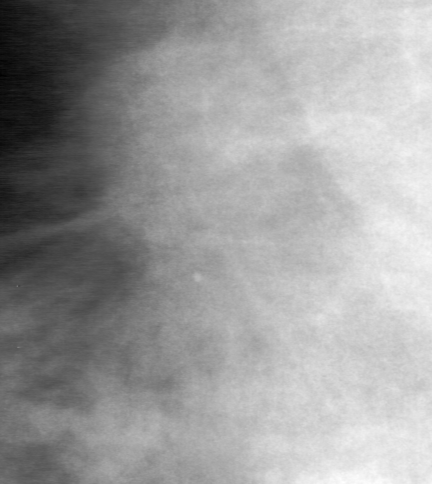
Region of interest cut from a scanned film mammogram (one marked finding), right breast, MLO view.
Finding: mass, shape round, margins spiculated; BI-RADS assessment category 3; subtlety rating 3 on a 1 (subtle) to 5 (obvious) scale; pathology (as recorded): malignant.